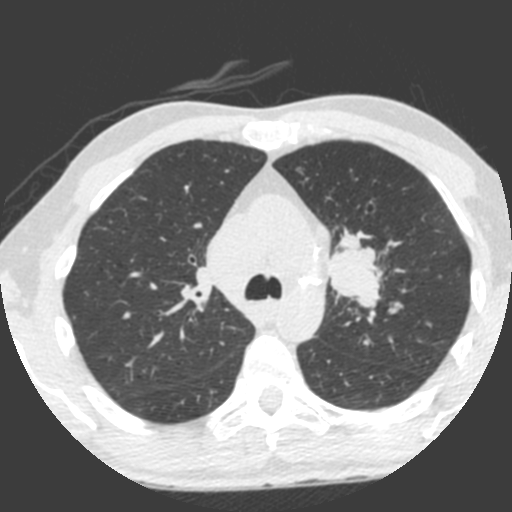
Axial slice from a low-dose chest CT screening exam; third annual screen; lung window (W 1500 / L -600 HU); 2 mm slice thickness; standard (soft-tissue) reconstruction kernel (B); slice 150 of 212 in the series. Male participant, aged 55 years at enrolment. Current smoker at enrolment.
Lesion marked by an expert reader, bounding box <308,231,390,323> (left, top, right, bottom; pixels). Screening reader's record for this exam (one nodule recorded; not confirmed to be the boxed lesion): non-calcified nodule or mass ≥4 mm, left upper lobe, 49 × 29 mm, spiculated (stellate) margins, soft tissue attenuation, pre-existing on the prior screen: yes; interval growth: yes. Official screen result: positive, other. Lung cancer was diagnosed 0 days after this screen: small cell carcinoma, NOS, left upper lobe, undifferentiated (G4), stage IV (AJCC 6th edition), 60 mm at pathology.